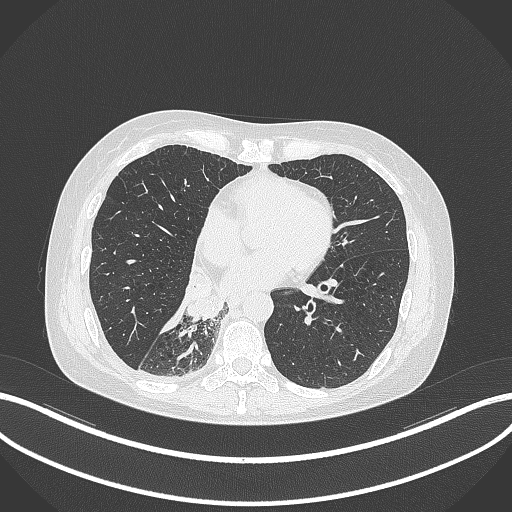
Chest CT, one axial slice. Slice 121 of 329 in the series (ordered by position). 120 kVp. Lung window (W 1500 / L -600 HU). 1 mm slice thickness. 512 × 512 image matrix, field of view 400 × 400 mm. Female patient, age 63 years. From the clinical record (not read from this slice): clinical TNM (as recorded): T1c N0 M0.
Annotated regions visible in this slice (rectangle marked by the reading radiologist):
- lung tumour (recorded histology: adenocarcinoma): bounding box [x1, y1, x2, y2] px = [185, 268, 223, 324]